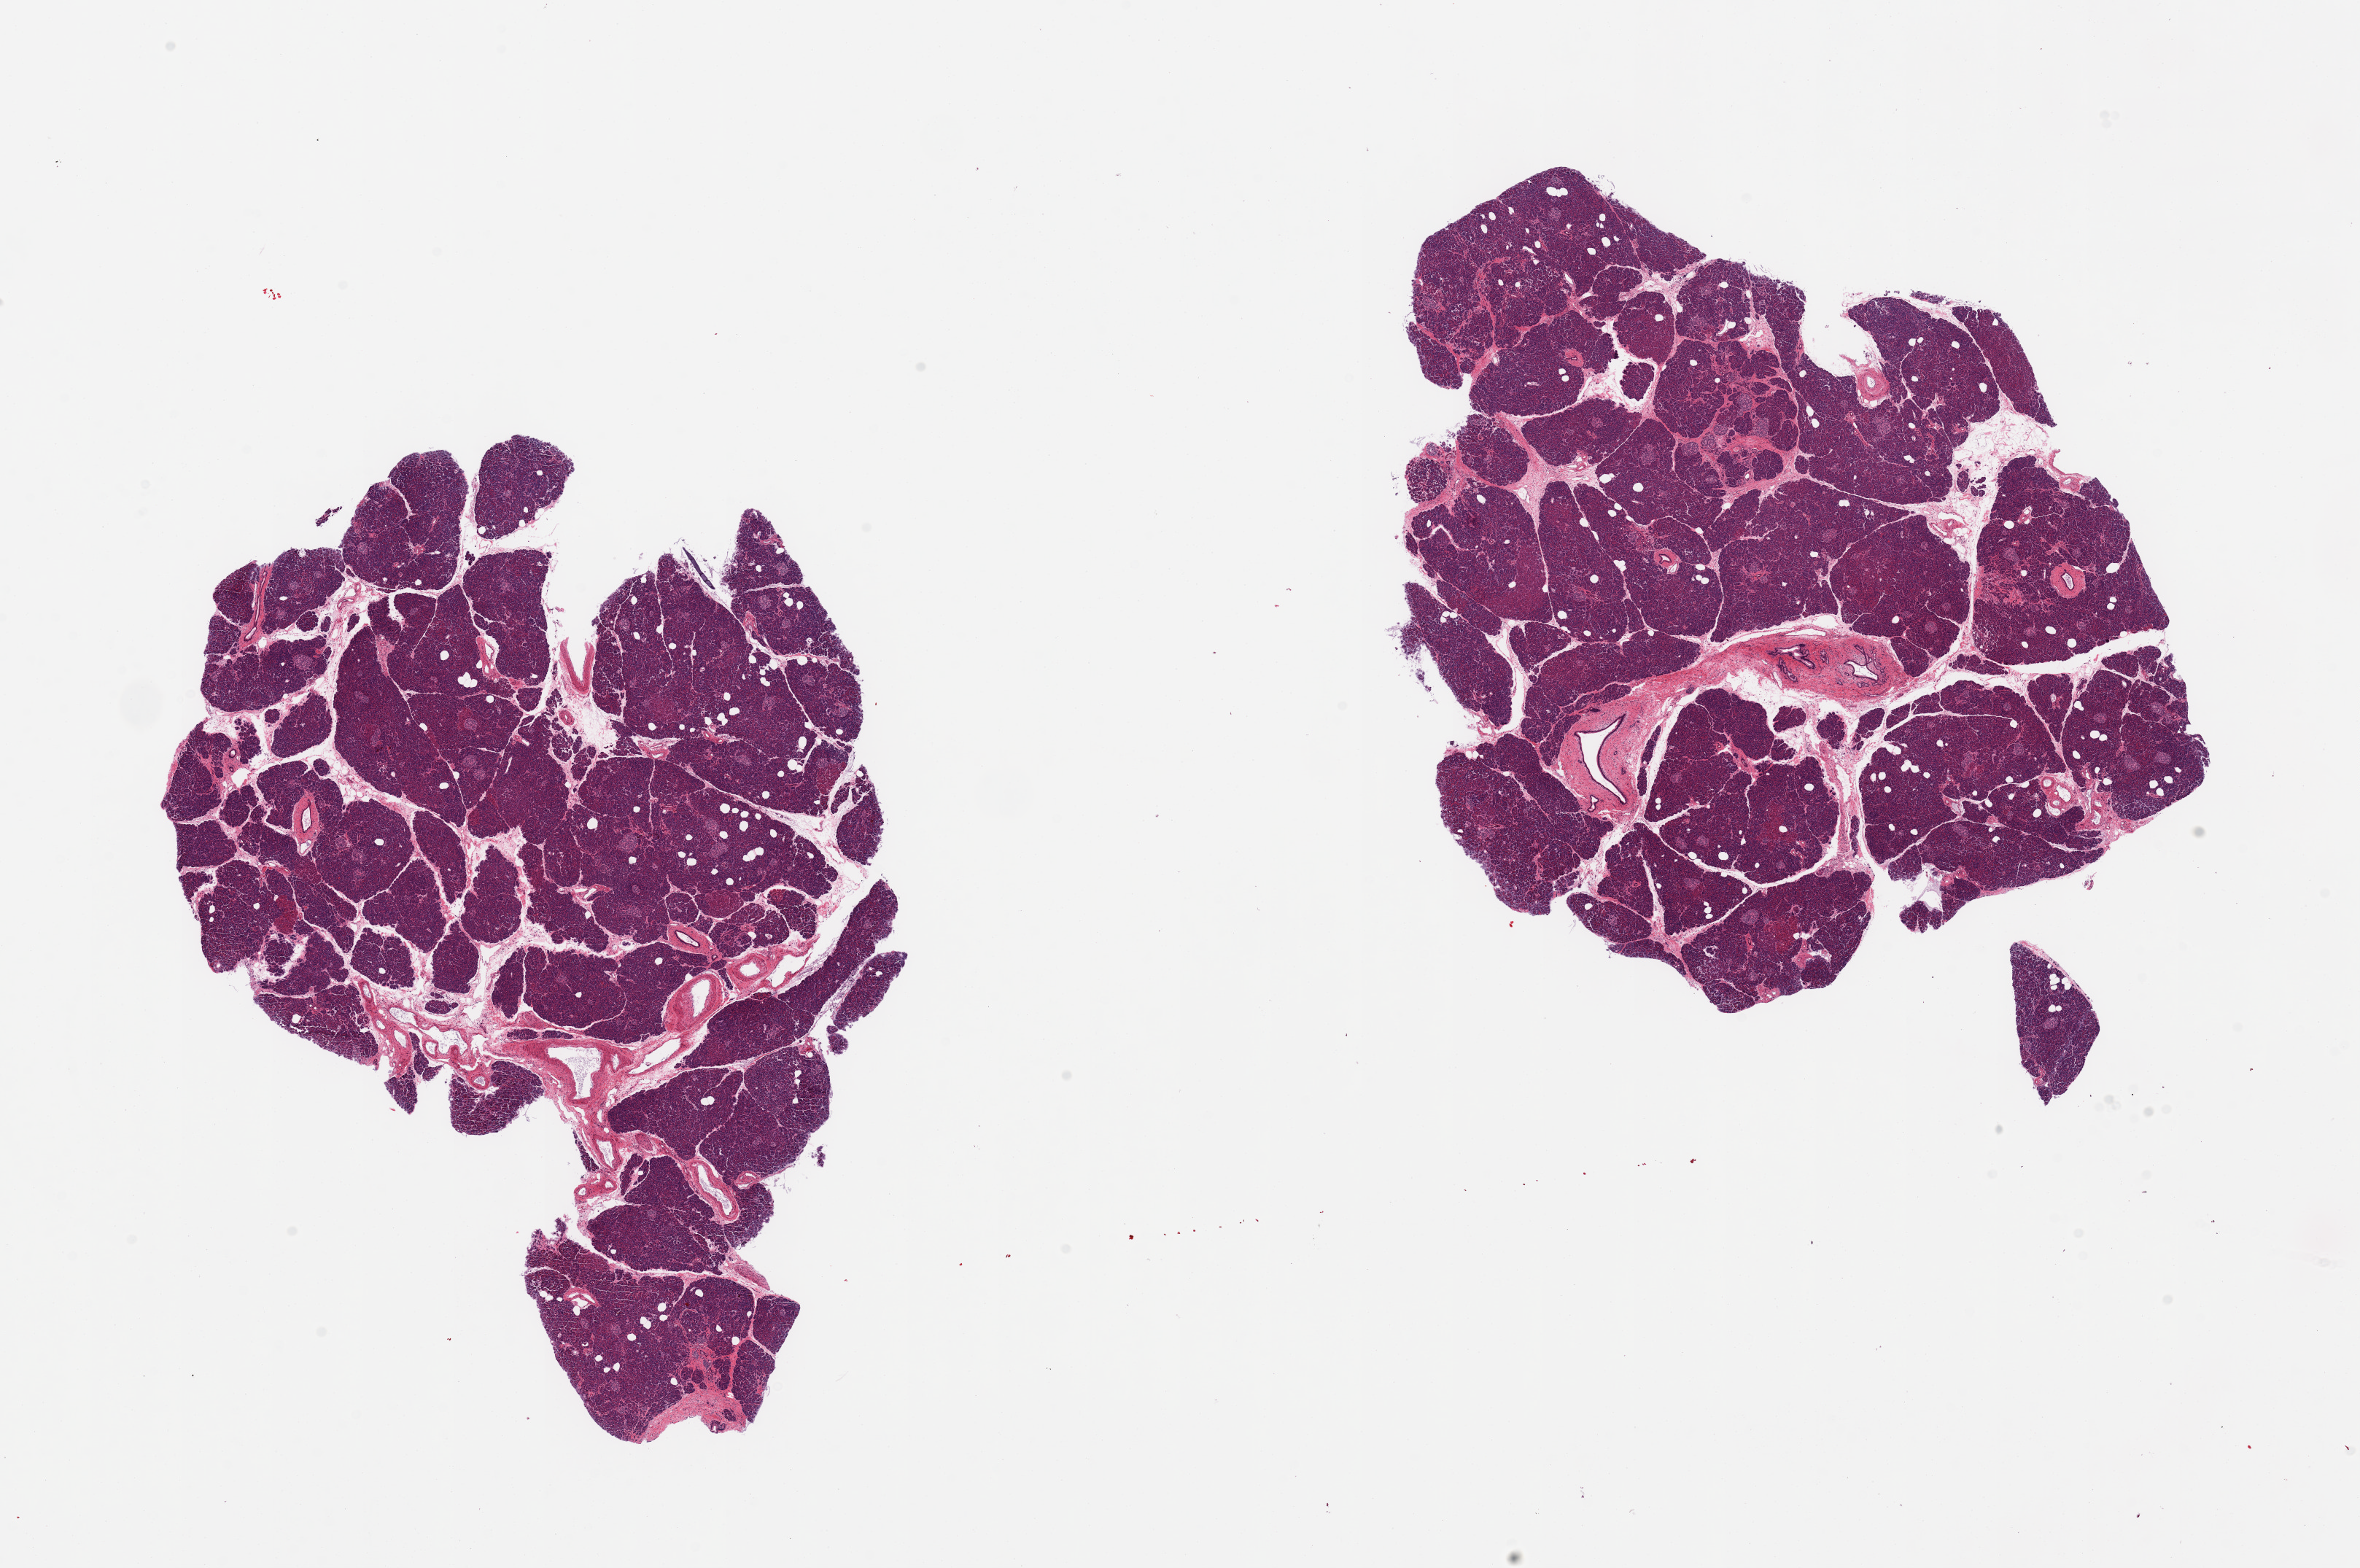
Hematoxylin and eosin (H&E) whole-slide image — shown as a low-resolution overview of the whole scanned area (about 25.6 x 17.0 mm). PAXgene-fixed paraffin-embedded (PFPE) section. Sampled site (target tissue): pancreas. Donor tissue sample. Donor sex: male.
* reviewer comment on this tissue sample: 2 pieces, well preserved, Islets well- visualized